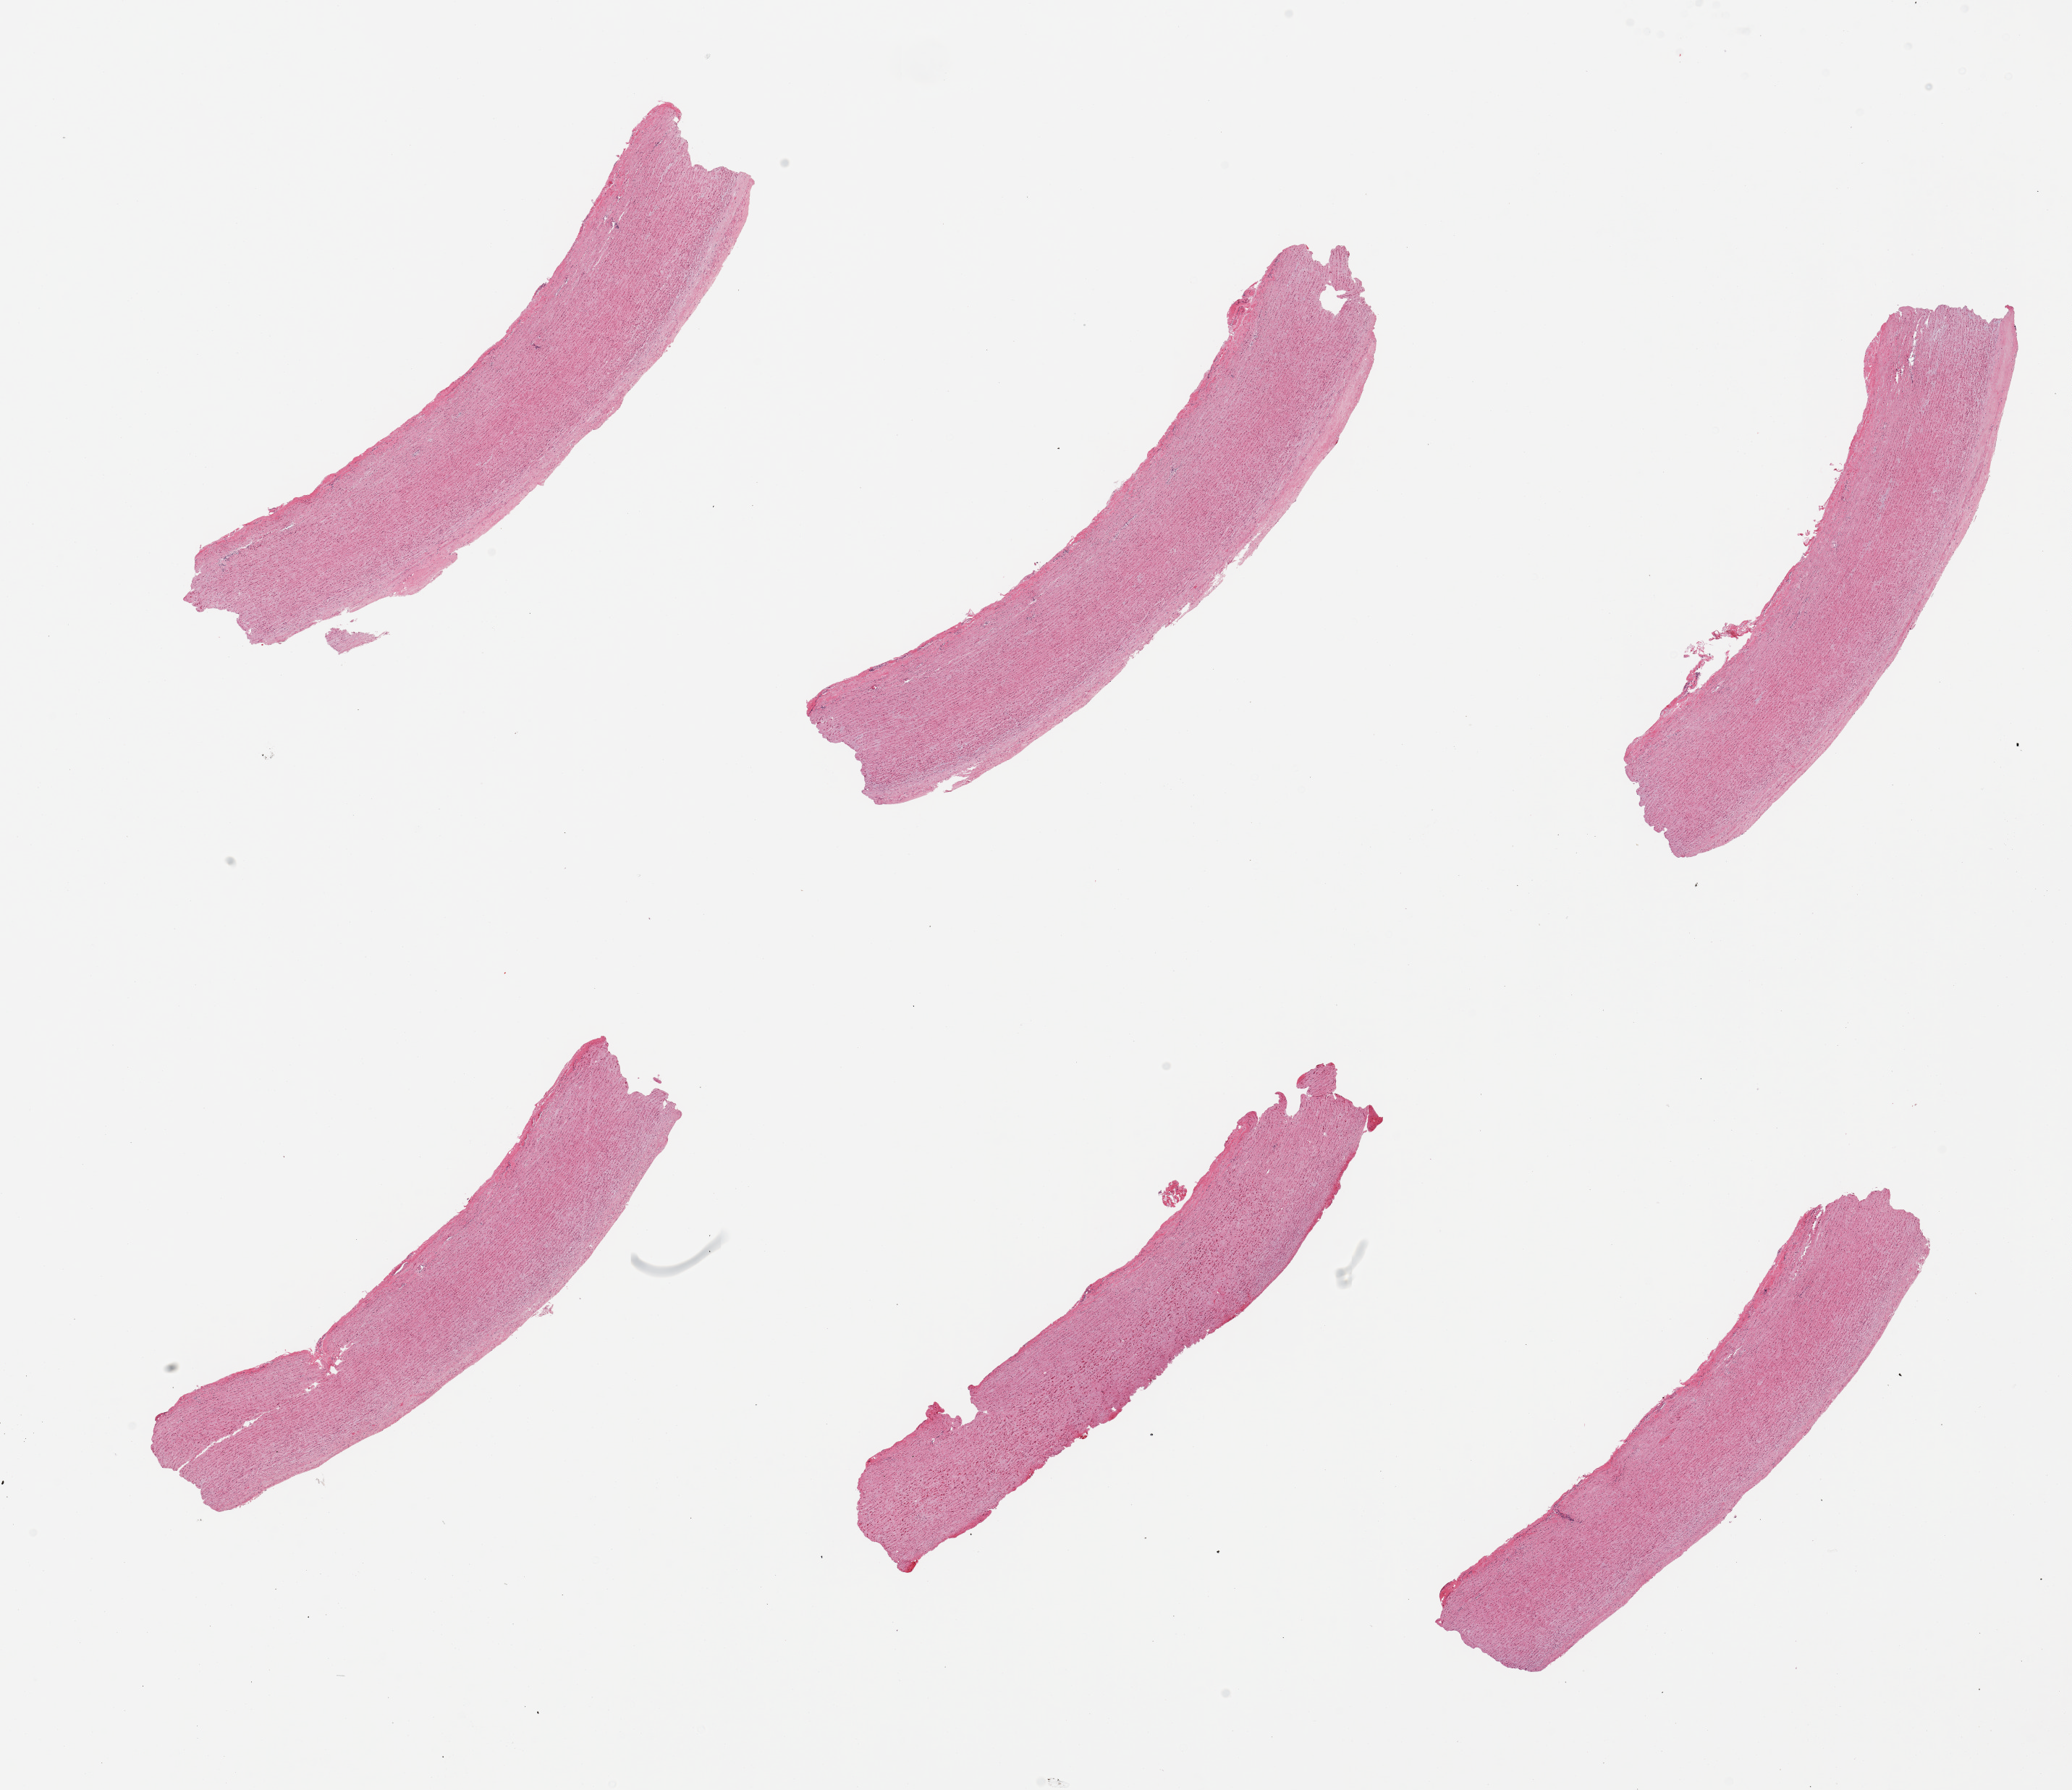
H&E whole-slide image, brightfield — a low-resolution overview of the entire scanned area, about 22.6 x 19.6 mm (acquisition: 20x scan), PAXgene-fixed, paraffin-embedded tissue, section of aorta (target tissue), donor tissue sample. Donor sex: male.
Review note (as recorded): 6 pieces; early plaque formation.